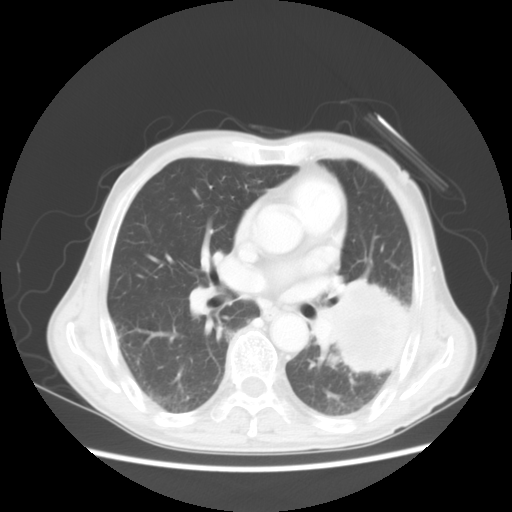
Chest CT, one axial slice. Slice 26 of 51 in the series (ordered by position). Lung window (W 1500 / L -600 HU). 512 × 512 image matrix, field of view 360 × 360 mm. Patient: male, 64 years. From the clinical record (not read from this slice): clinical TNM (as recorded): T4 N0 M0.
Structures marked on this image (bounding box drawn by a radiologist):
- lung tumour (recorded histology: squamous cell carcinoma): bounding box (x1, y1, x2, y2) in pixels: (324, 274, 426, 382)